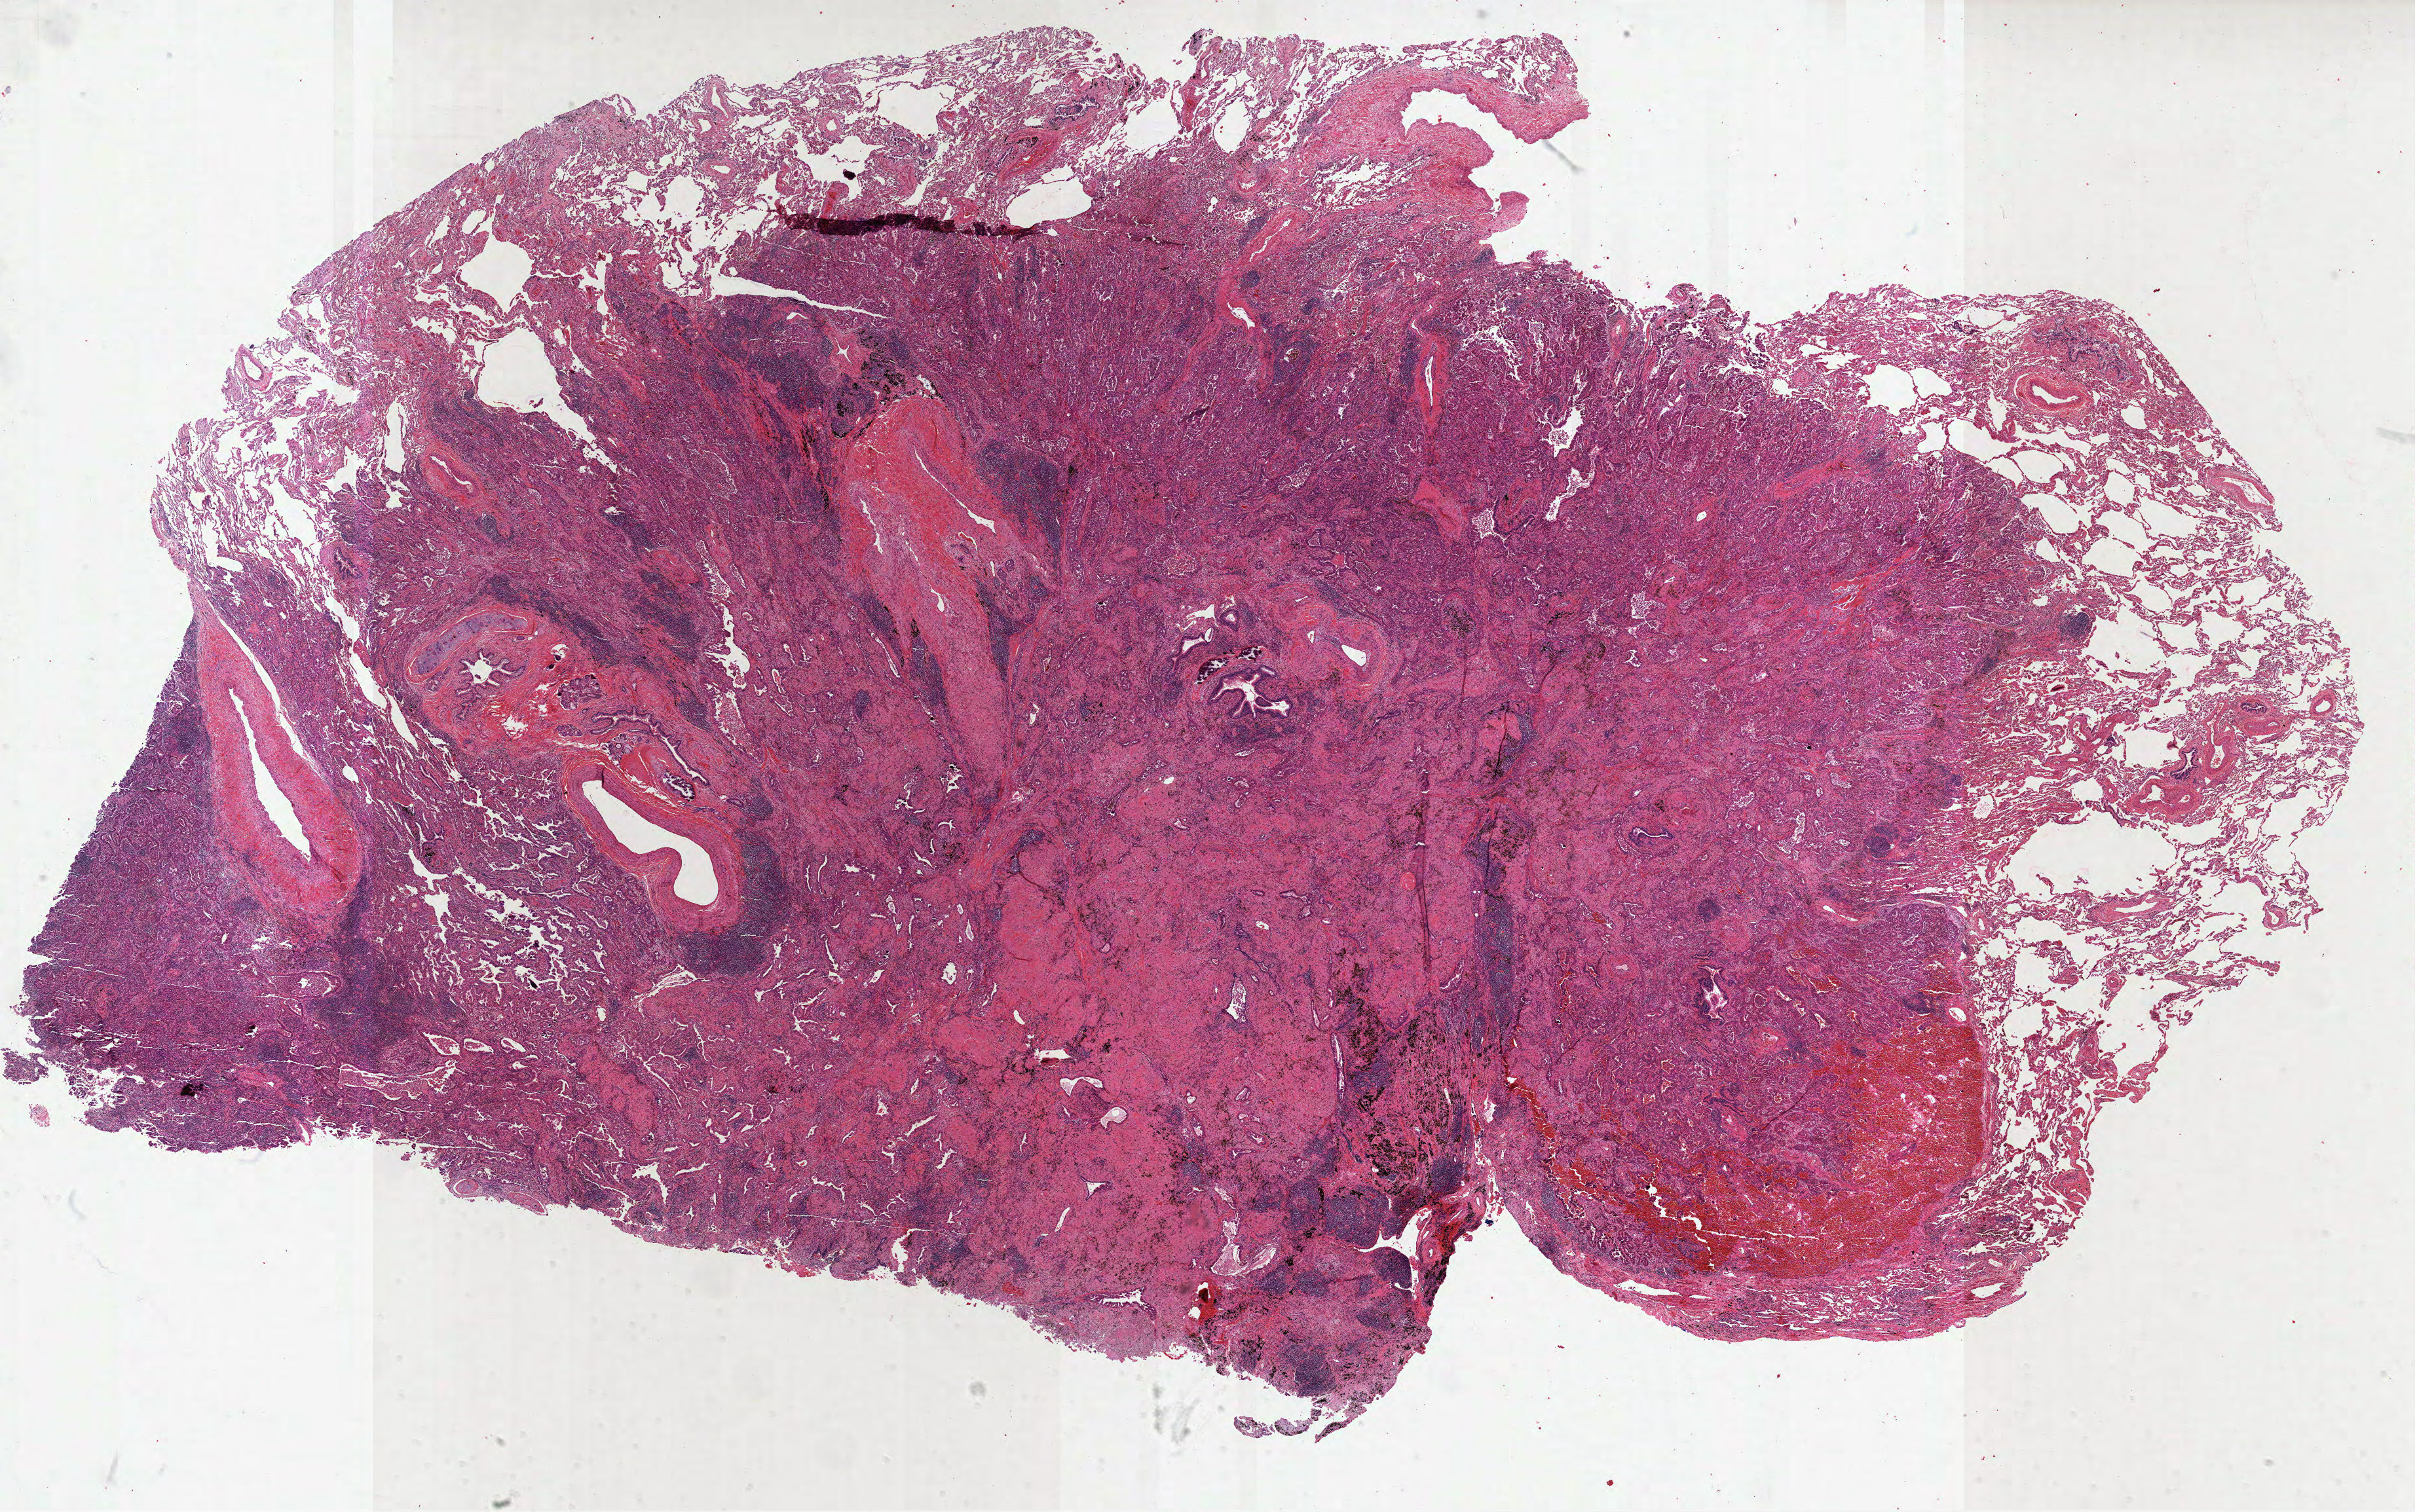
Digitized Hematoxylin and eosin (H&E) stained tissue section (whole slide) — a low-resolution overview of the entire scanned area, about 29.7 x 18.6 mm. Formalin-fixed paraffin-embedded (FFPE) diagnostic section. Sample: primary tumour, lung. Female patient; age at initial diagnosis 59 years.
Histologic diagnosis: Adenocarcinoma, NOS (lower lobe, lung). Laterality: right. AJCC pathologic stage: IIB.